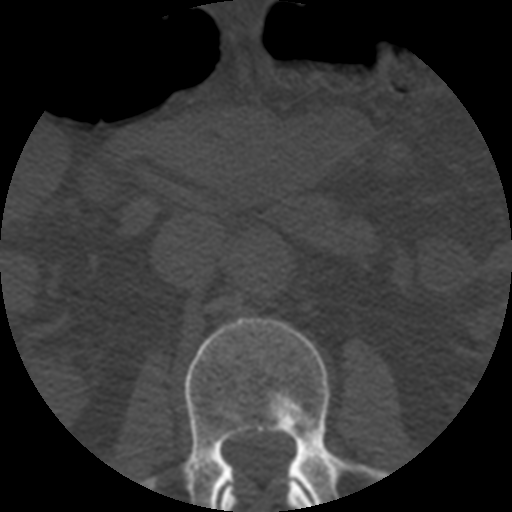
CT including the spine, one axial slice; slice 159 of 508 in the series (ordered by position); 120 kVp; bone window (W 1800 / L 400 HU); 512 × 512 image matrix, field of view 160 × 160 mm. Patient age 57 years. From the clinical record (not read from this slice): primary cancer: prostate.
Outlined on this slice (semi-automatic segmentation, software-assisted and operator-edited):
- L1 vertebra: bounding box (x1, y1, x2, y2) in pixels: (219, 482, 314, 512)
- L2 vertebra: (143, 317, 387, 512)